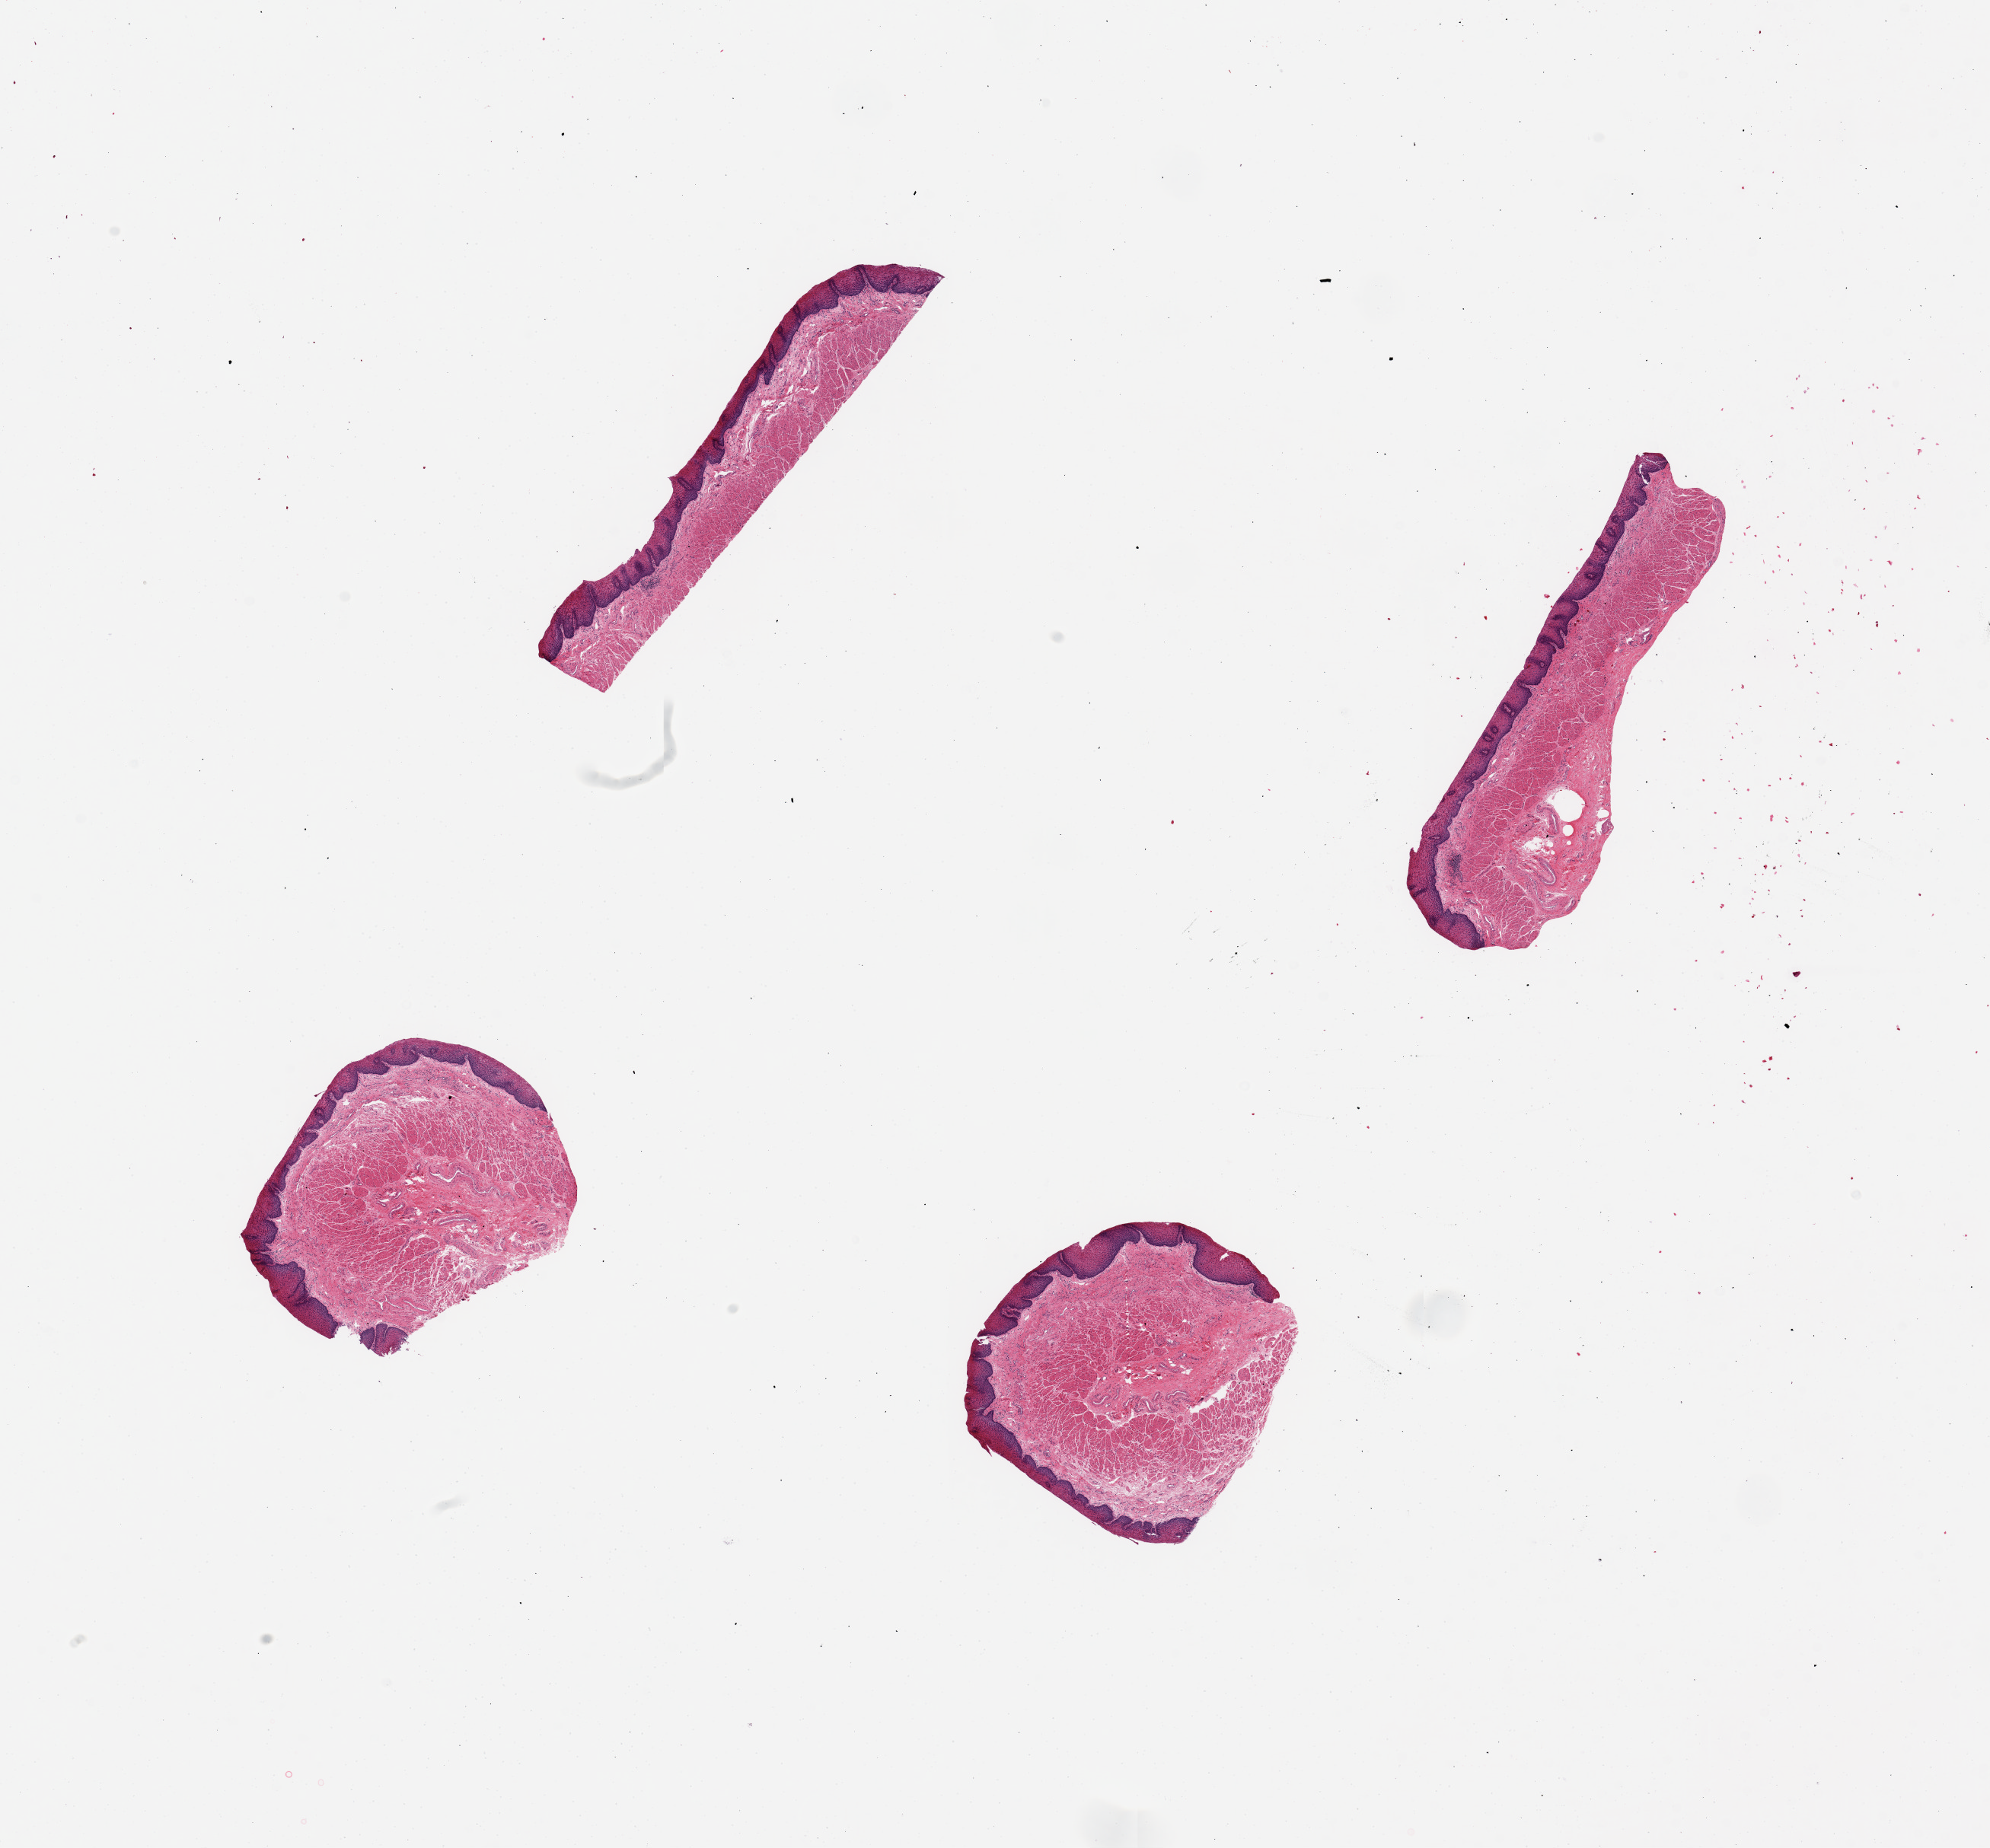
Digitized hematoxylin and eosin (H&E)-stained section — a low-resolution overview of the entire scanned area, about 20.7 x 19.2 mm, PAXgene-fixed paraffin-embedded (PFPE) section, target tissue: gastroesophageal junction, donor tissue sample. Donor sex: male.
Reviewer comment on this tissue sample: 4 pieces, up to 6x1mm; All mucosa and thickened muscularis mucosa; no muscularis propria.